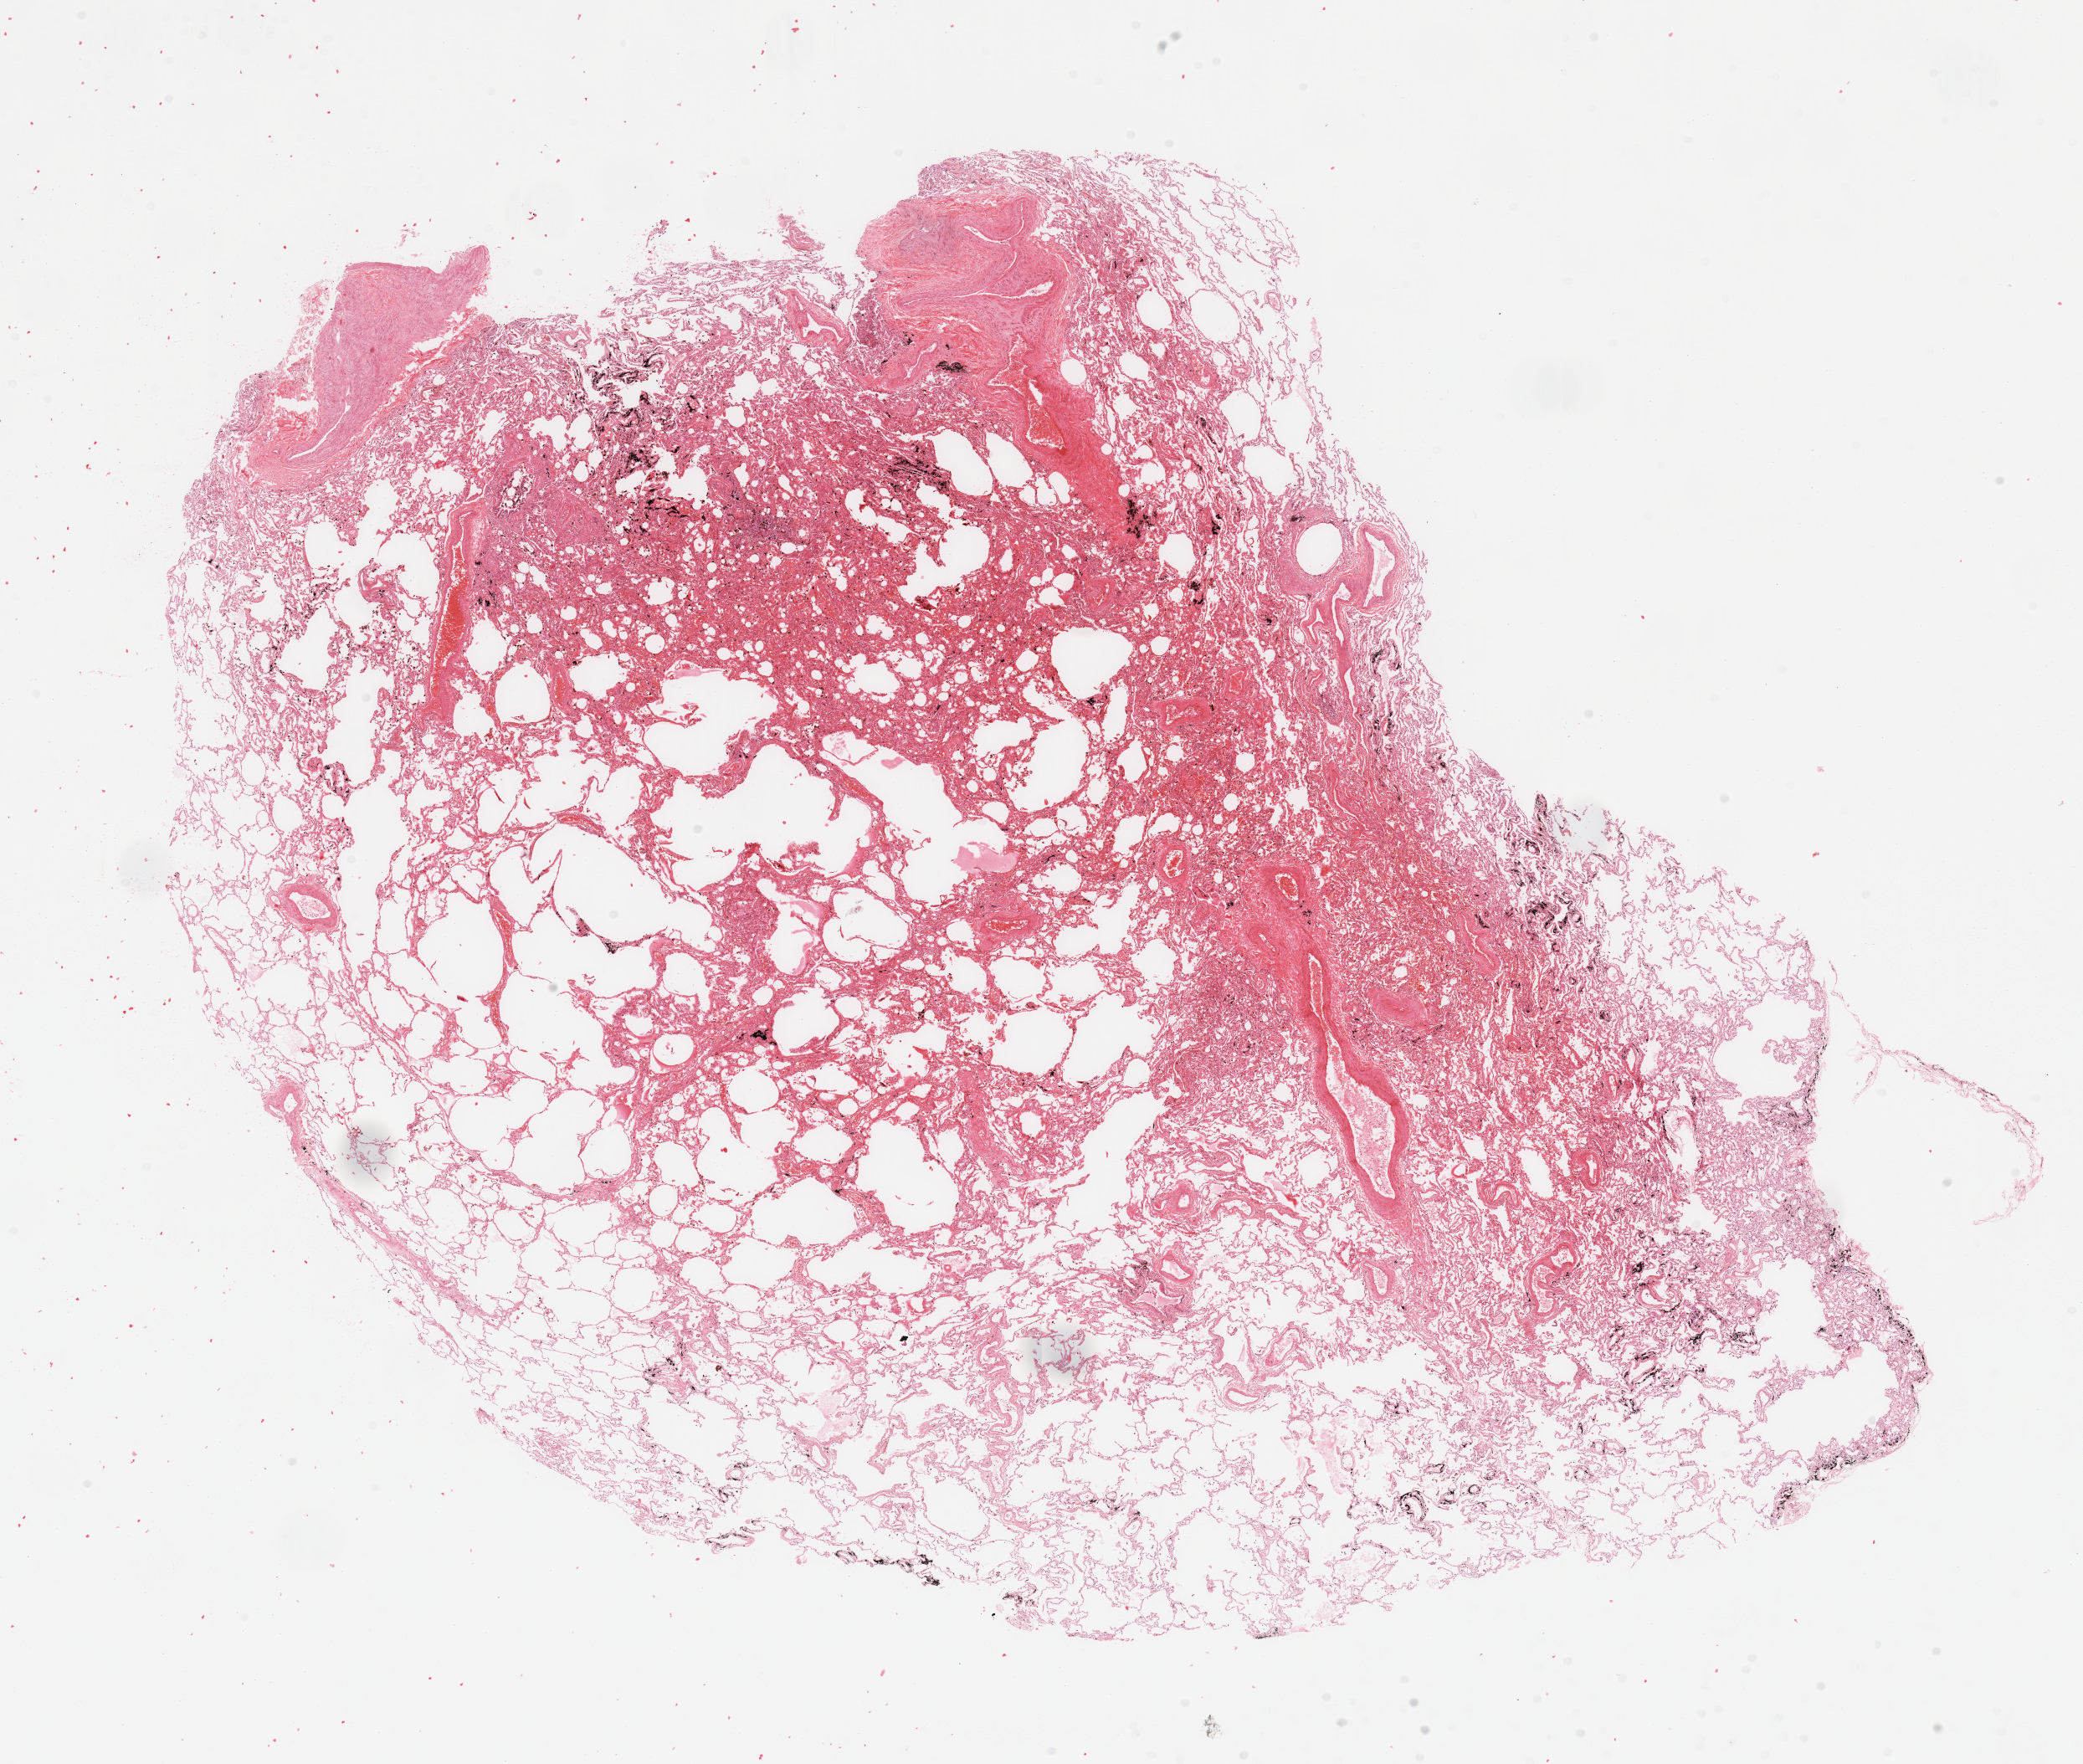
Hematoxylin and eosin (H&E) stained whole-slide image, a low-resolution overview of the entire scanned area, about 19.7 x 16.7 mm. Normal (non-tumour) tissue sample, sampled site: lung. Patient: male, age 72 years.
- this section: normal (non-tumour) tissue from the same patient
- patient diagnosis: Adenocarcinoma, NOS